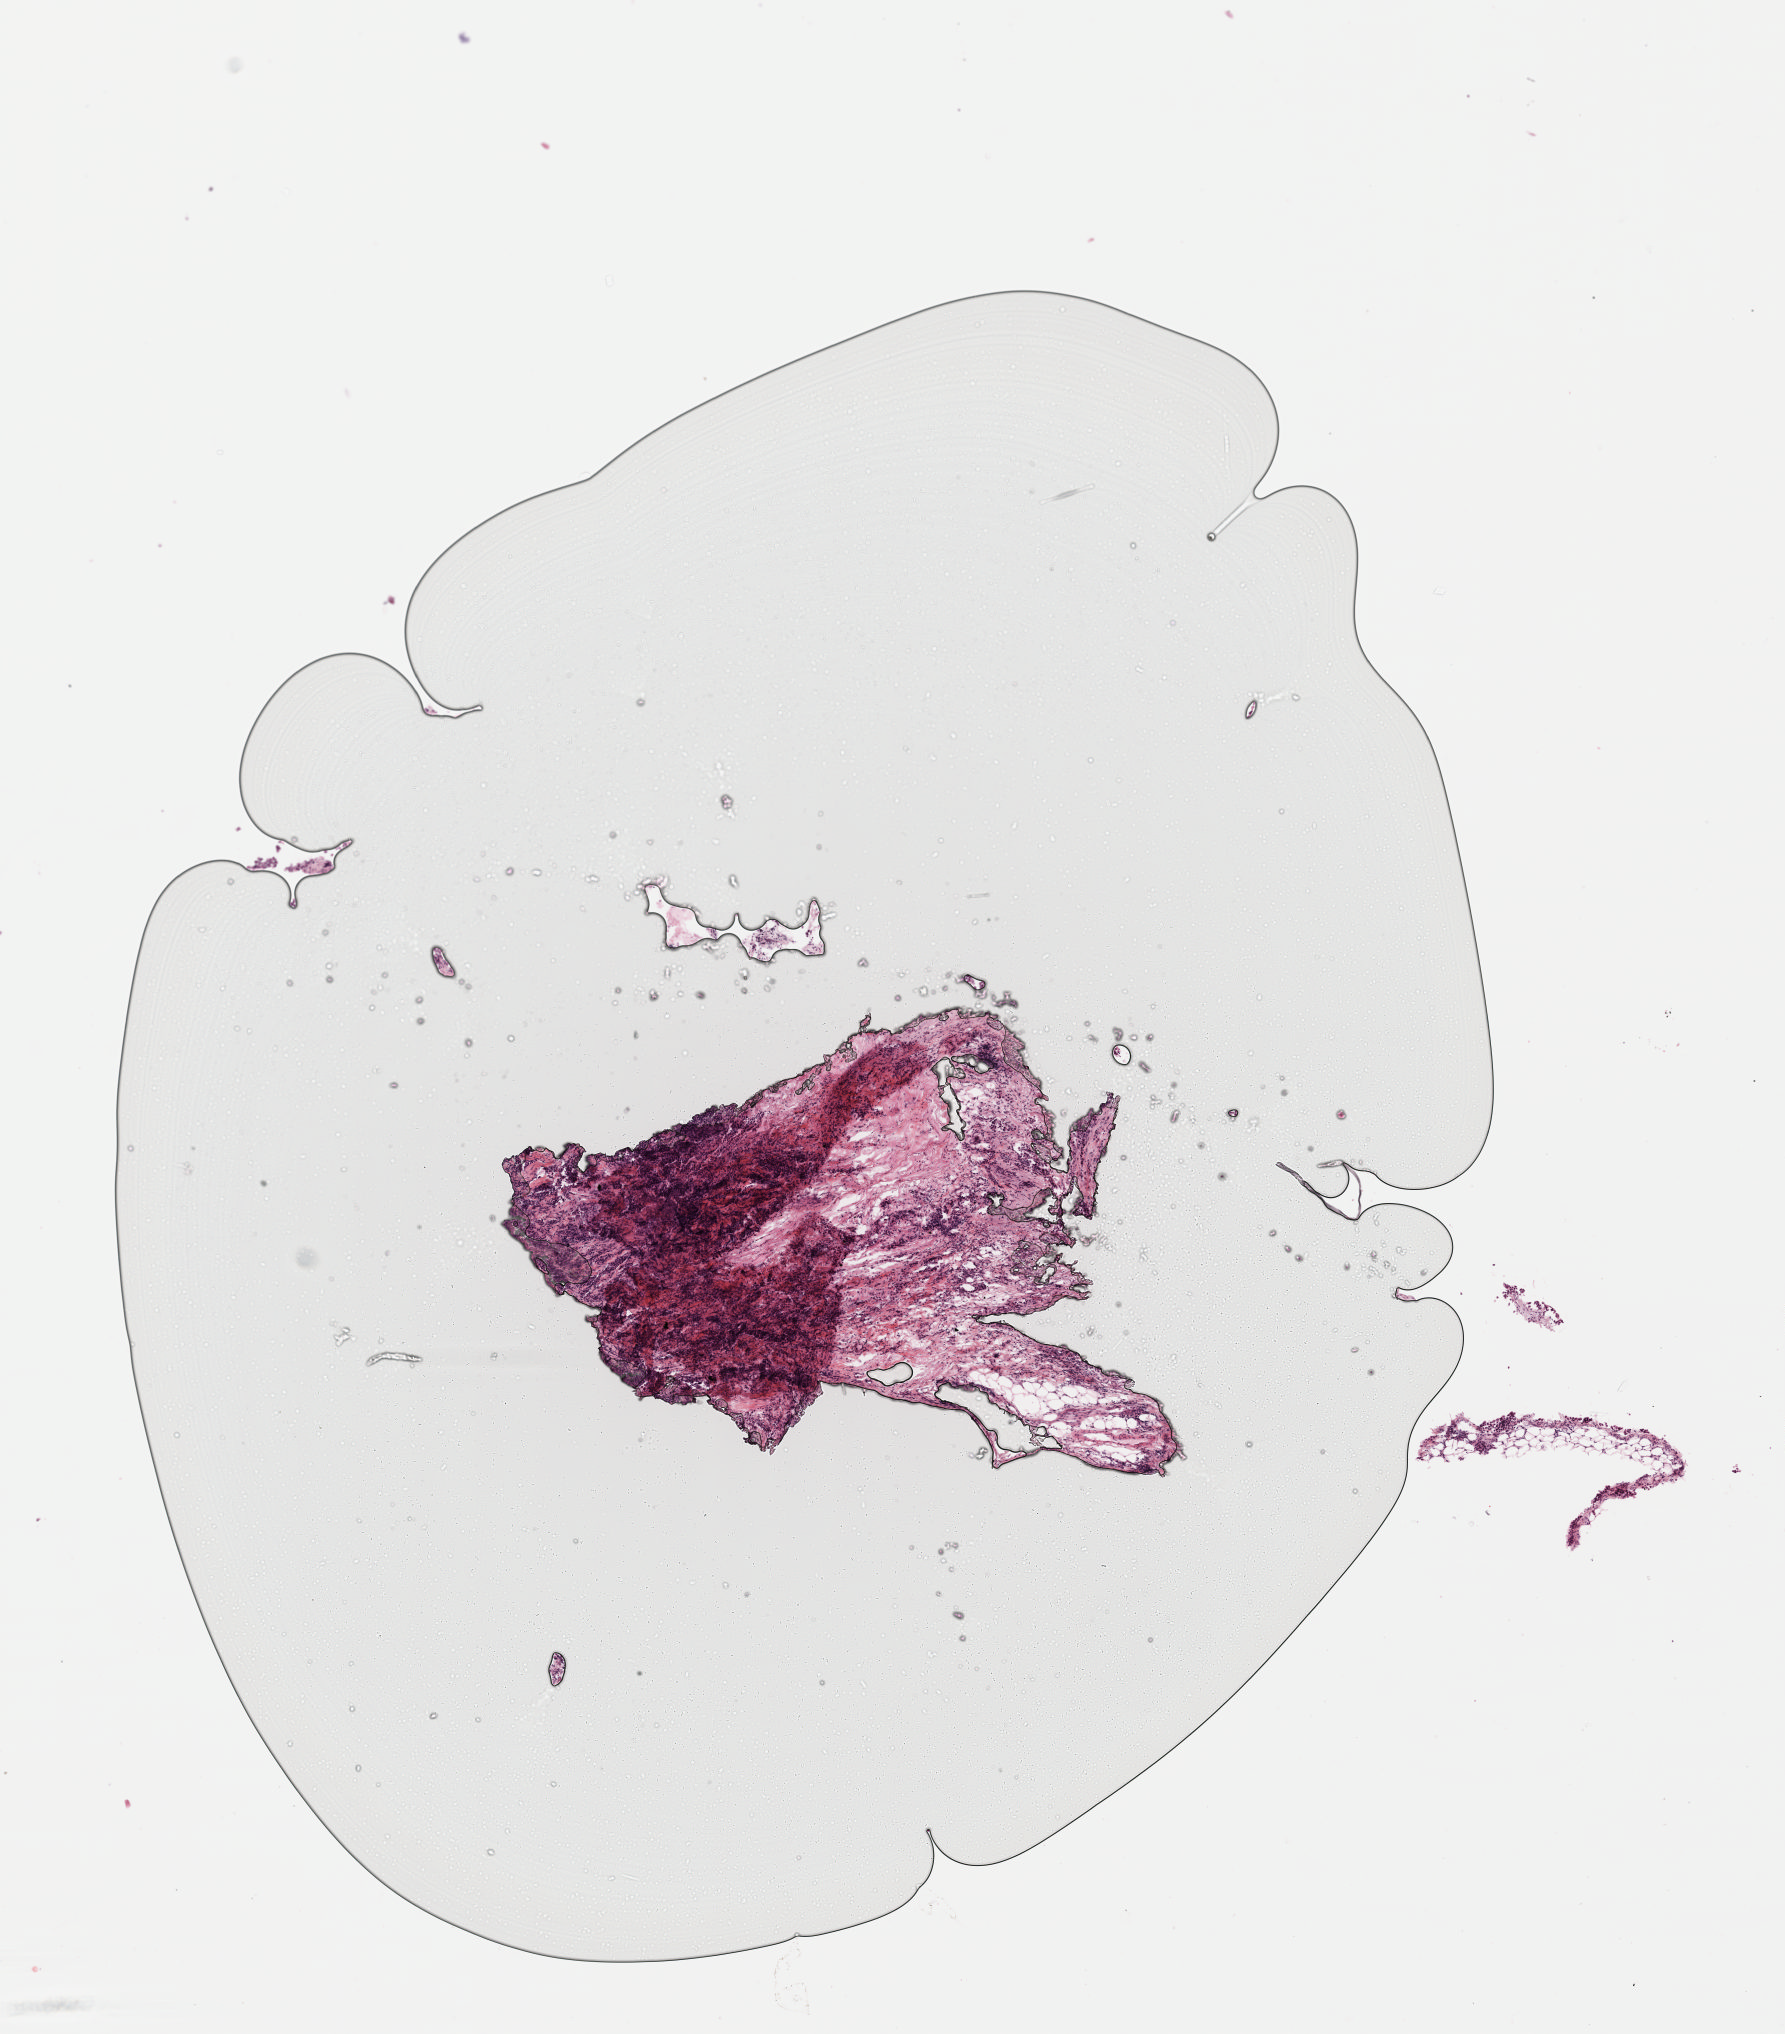
H&E-stained whole-slide image, a low-resolution overview of the entire scanned area, about 7.0 x 8.0 mm (slide scanned at 40x); formalin-fixed paraffin-embedded (FFPE) diagnostic section; primary tumour sample from the mesothelium. Patient: female, age at initial diagnosis 73 years.
Laterality: right. AJCC pathologic stage: III (6th edition). Pathologic diagnosis: Epithelioid mesothelioma, malignant (pleura, NOS). TNM: T2 N1 MX.